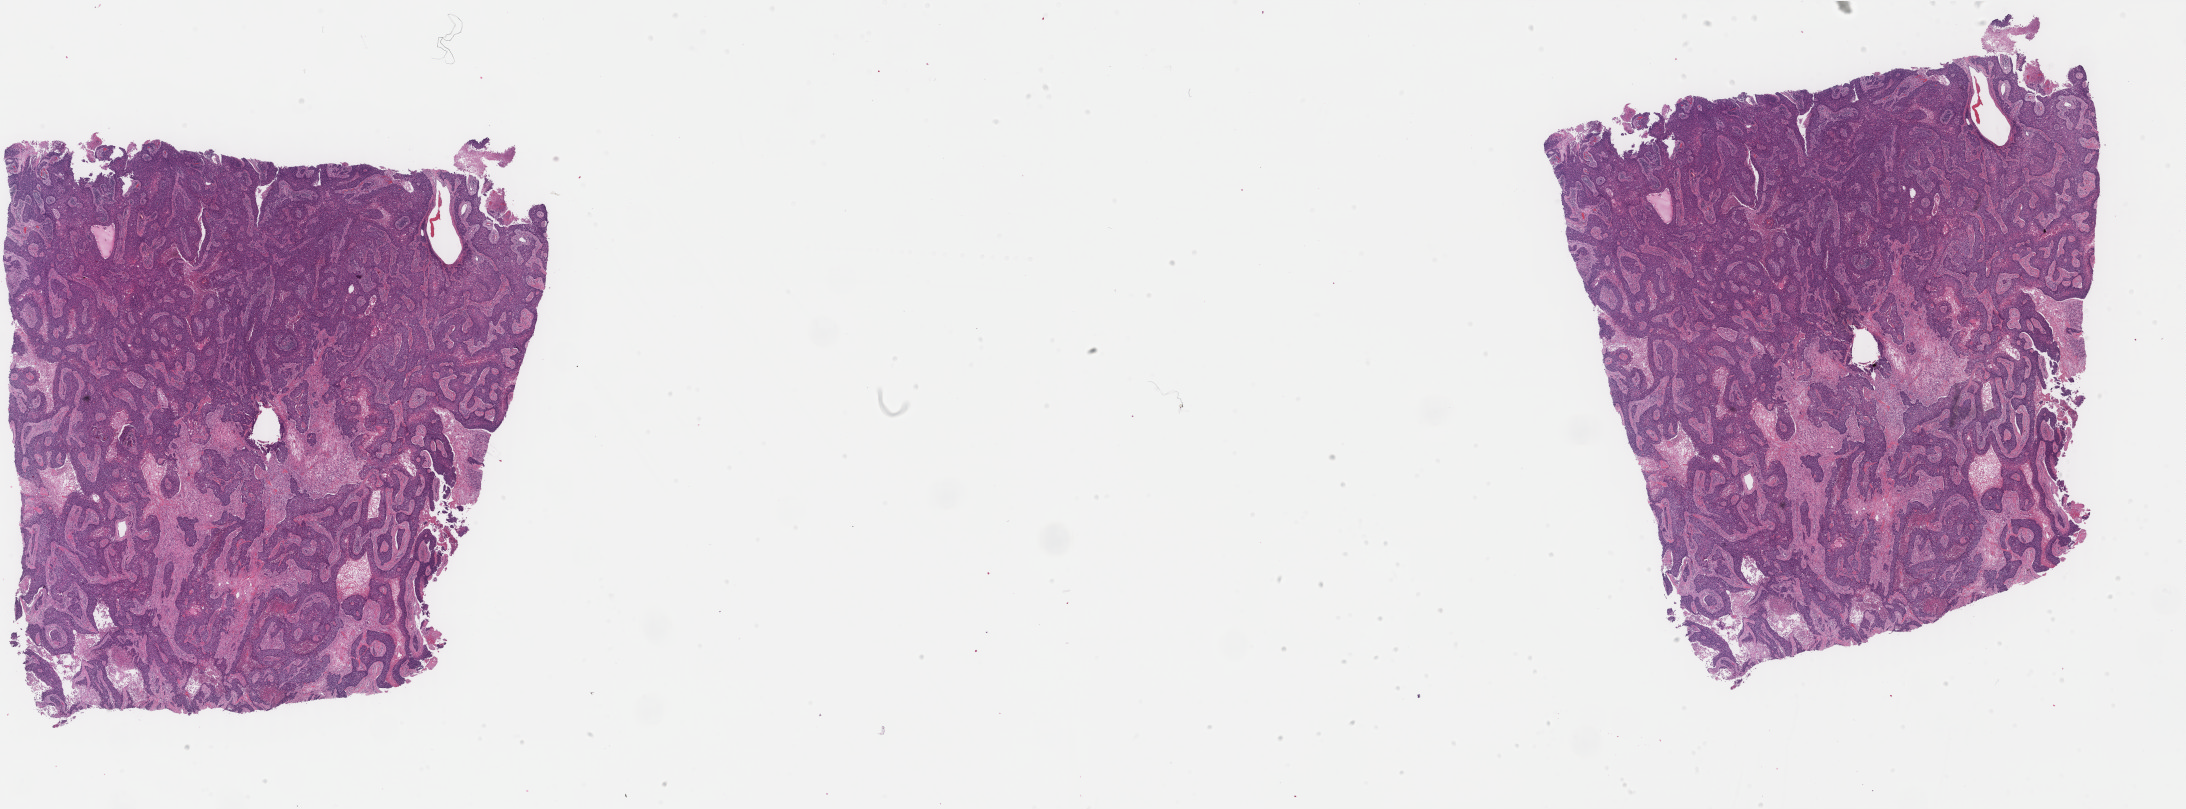
H&E-stained whole-slide image — low-resolution overview of the scanned area, about 34.7 x 12.8 mm (from a 40x scan). Formalin-fixed paraffin-embedded (FFPE) diagnostic section. Primary tumour sample from the breast. Patient: female, age at initial diagnosis 59 years.
- diagnosis: Infiltrating duct carcinoma, NOS
- AJCC pathologic stage: IV
- lymph nodes positive (case pathology): 8 of 14 examined